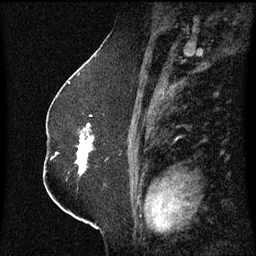
Breast MRI (dynamic contrast-enhanced), one sagittal slice. Position 34 of 60 along the scan axis. Dynamic contrast-enhanced series, image 2 of 3 at this slice position (ordered by acquisition). 1.5 T. TE 4.2 ms, TR 8.4 ms. 2.3 mm slice thickness. 256 × 256 image matrix. Female patient, age 52 years. From the clinical record (not read from this slice): setting: breast cancer imaged before/during neoadjuvant chemotherapy; receptor status: HR-positive, HER2-negative.
Annotated regions visible in this slice (semi-automatically segmented with operator editing):
- analysis volume of interest (the breast-tissue region the enhancement analysis was run in; not a lesion): bounding box <77,116,110,179> (left, top, right, bottom; pixels)
- tumour enhancement mask (voxels above the 70 % enhancement threshold inside the analysis volume of interest): <77,124,94,175>